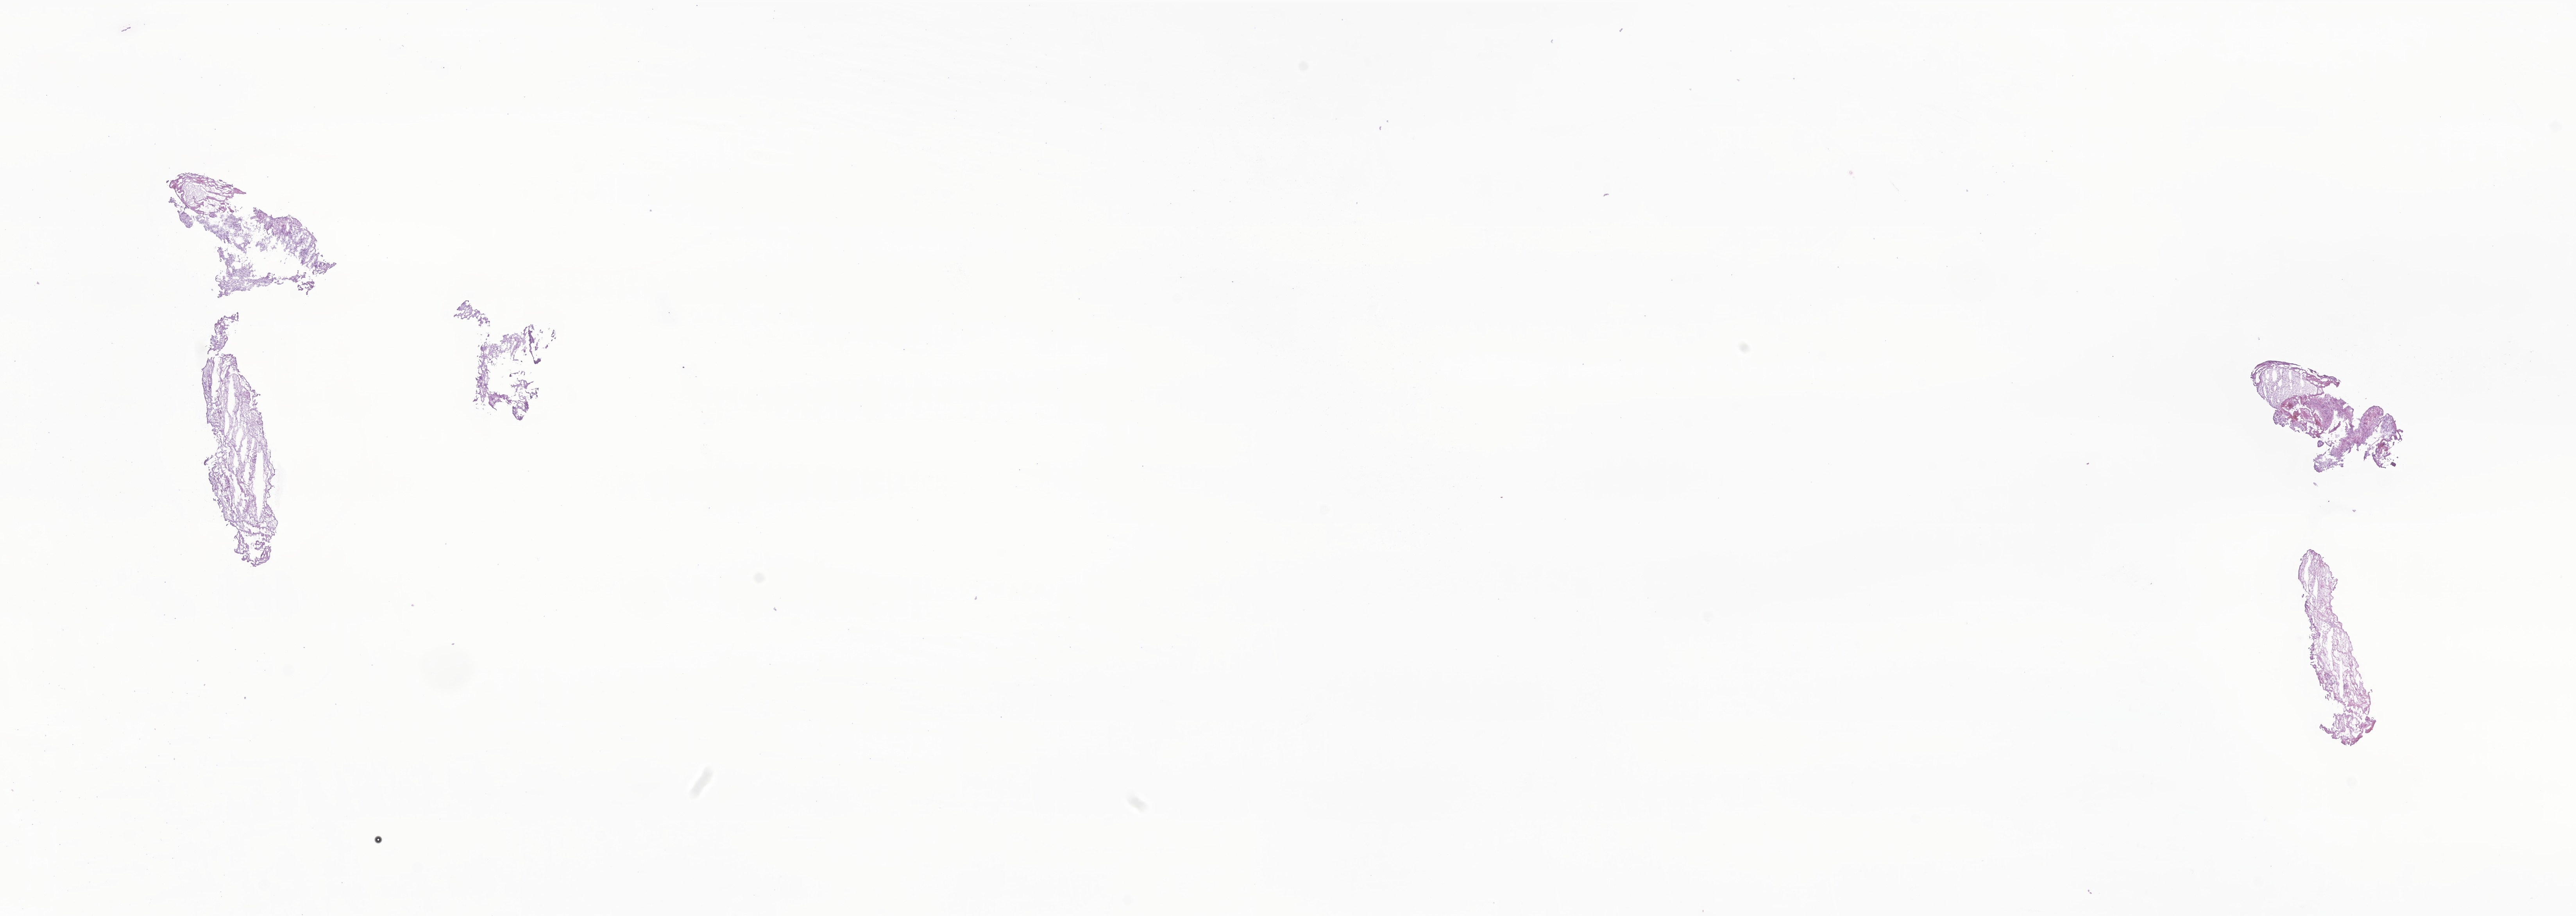
Hematoxylin and eosin (H&E) whole-slide image of tumor tissue from the brain stem, whole scanned area (about 27.8 x 9.9 mm) shown as a low-resolution overview; frozen section (OCT-embedded). Male patient, age 58 months (4 years 10 months).
Diagnosis (ICD-O-3 morphology term): Glioma, malignant.